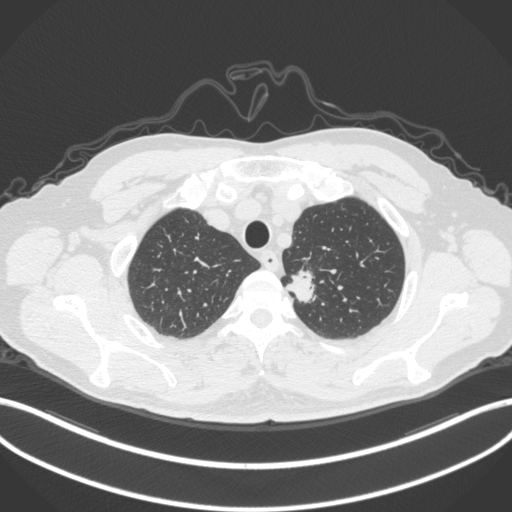
Chest CT, one axial slice; position 320 of 382 along the scan axis; reconstruction kernel B31f; 120 kVp; lung window (W 1500 / L -600 HU); 1 mm slice thickness; 512 × 512 image matrix, field of view 400 × 400 mm. Male patient, age 64 years. Case-level facts recorded for this patient, not image findings: clinical TNM (as recorded): T1c N0 M0.
Structures marked on this image (bounding box drawn by a radiologist):
- lung tumour (recorded histology: adenocarcinoma): bounding box [x1, y1, x2, y2] px = [287, 268, 324, 307]